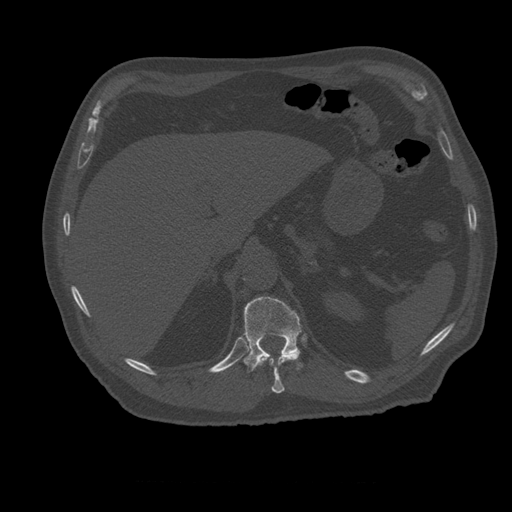
CT including the spine, one axial slice; position 267 of 399 along the scan axis; reconstruction kernel STANDARD; bone window (W 1800 / L 400 HU); 1.25 mm slice thickness; 512 × 512 image matrix, field of view 407 × 407 mm. Patient age 73 years. From the clinical record (not read from this slice): primary cancer: prostate; vertebrae with lytic lesions (as recorded): L2.
Annotated regions visible in this slice (semi-automatic segmentation, software-assisted and operator-edited):
- T11 vertebra: bounding box <258,352,301,394> (left, top, right, bottom; pixels)
- T12 vertebra: <244,297,303,372>